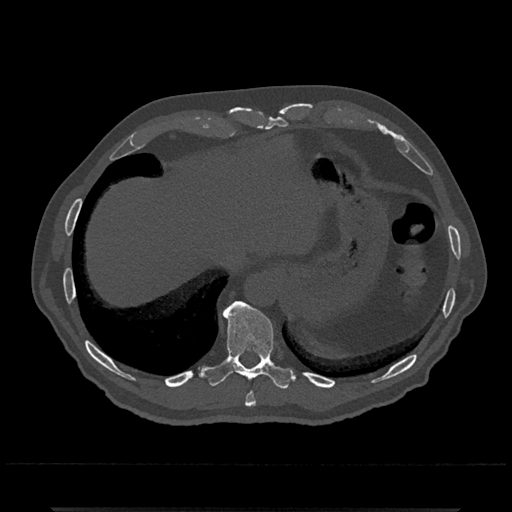
CT including the spine, one axial slice; position 559 of 797 along the scan axis; 120 kVp; bone window (W 1800 / L 400 HU); 0.5 mm slice thickness; 512 × 512 image matrix, field of view 393 × 393 mm. Patient: male, 67 years. Case-level facts recorded for this patient, not image findings: primary cancer: prostate.
Annotated regions visible in this slice (semi-automatically segmented with operator editing):
- T10 vertebra: bounding box [x1, y1, x2, y2] px = [203, 300, 294, 389]
- T9 vertebra: [245, 392, 256, 407]